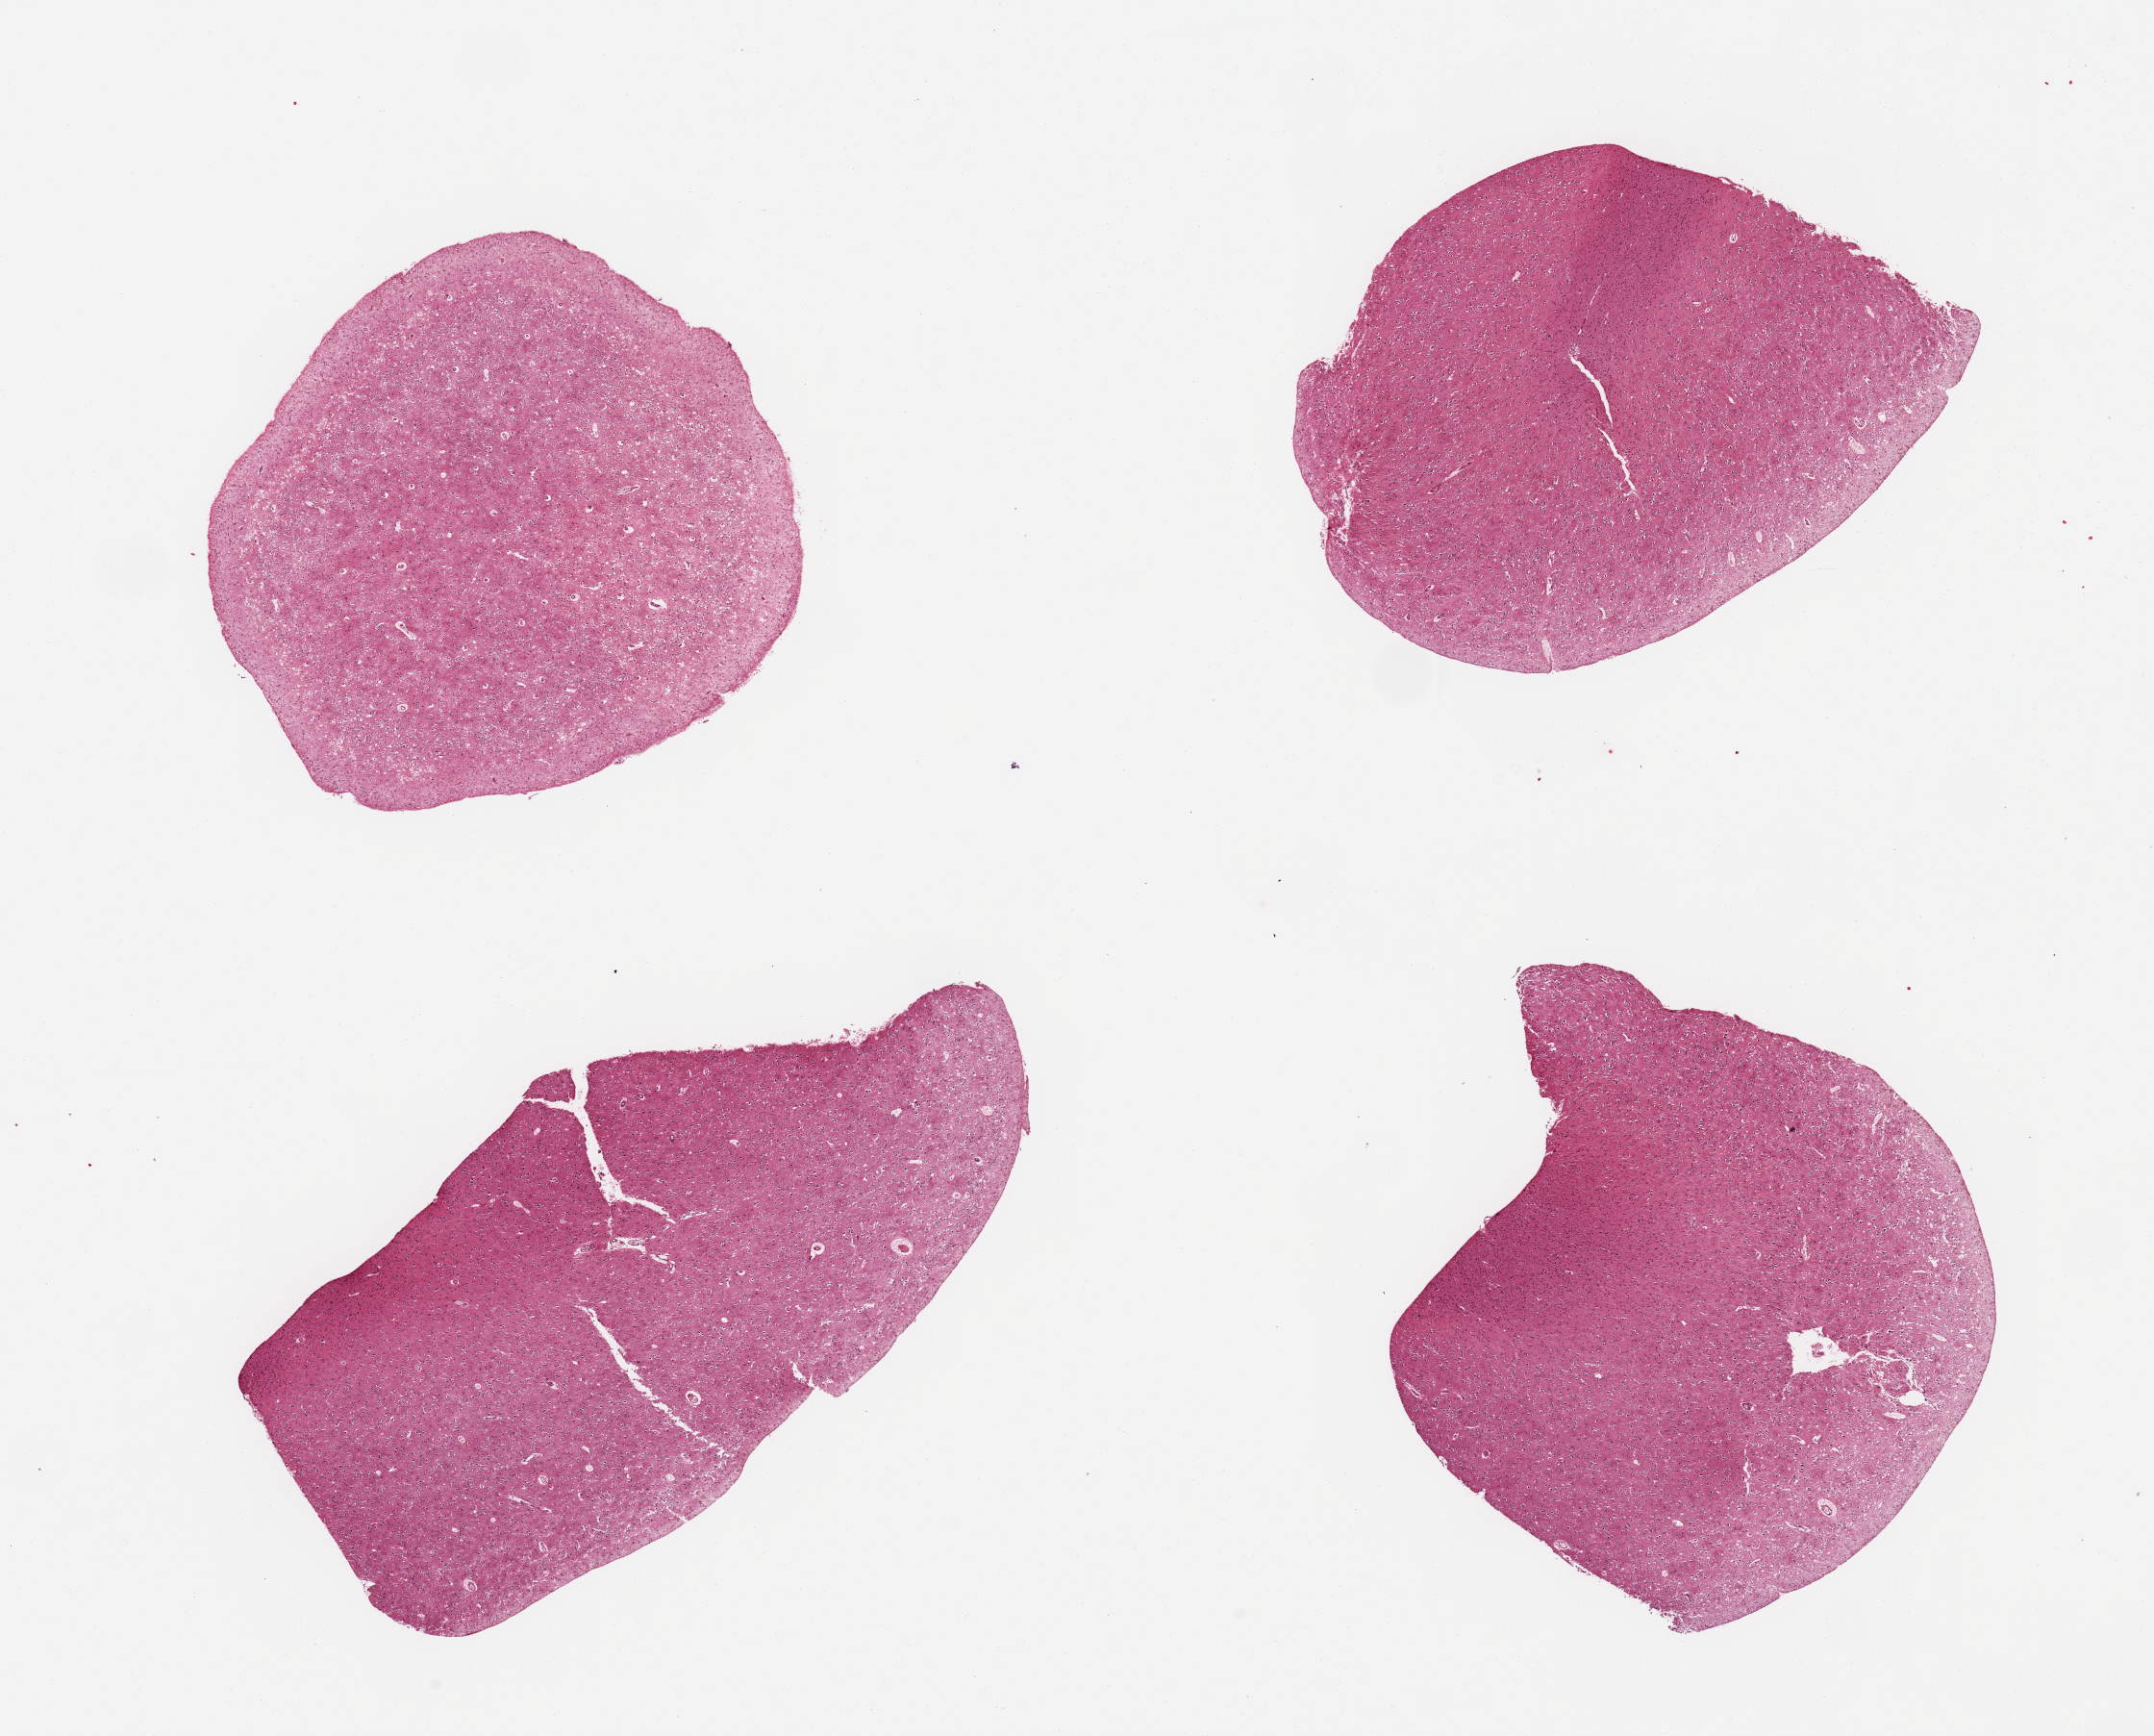
Whole-slide image, hematoxylin and eosin (H&E) stain — whole scanned area (about 17.7 x 14.3 mm, acquisition: 20x scan) shown as a low-resolution overview; PAXgene-fixed, paraffin-embedded tissue; sampled site (target tissue): cerebral cortex; tissue donor sample. Donor: male.
Review note (as recorded): 4 pieces, no abnormalities.